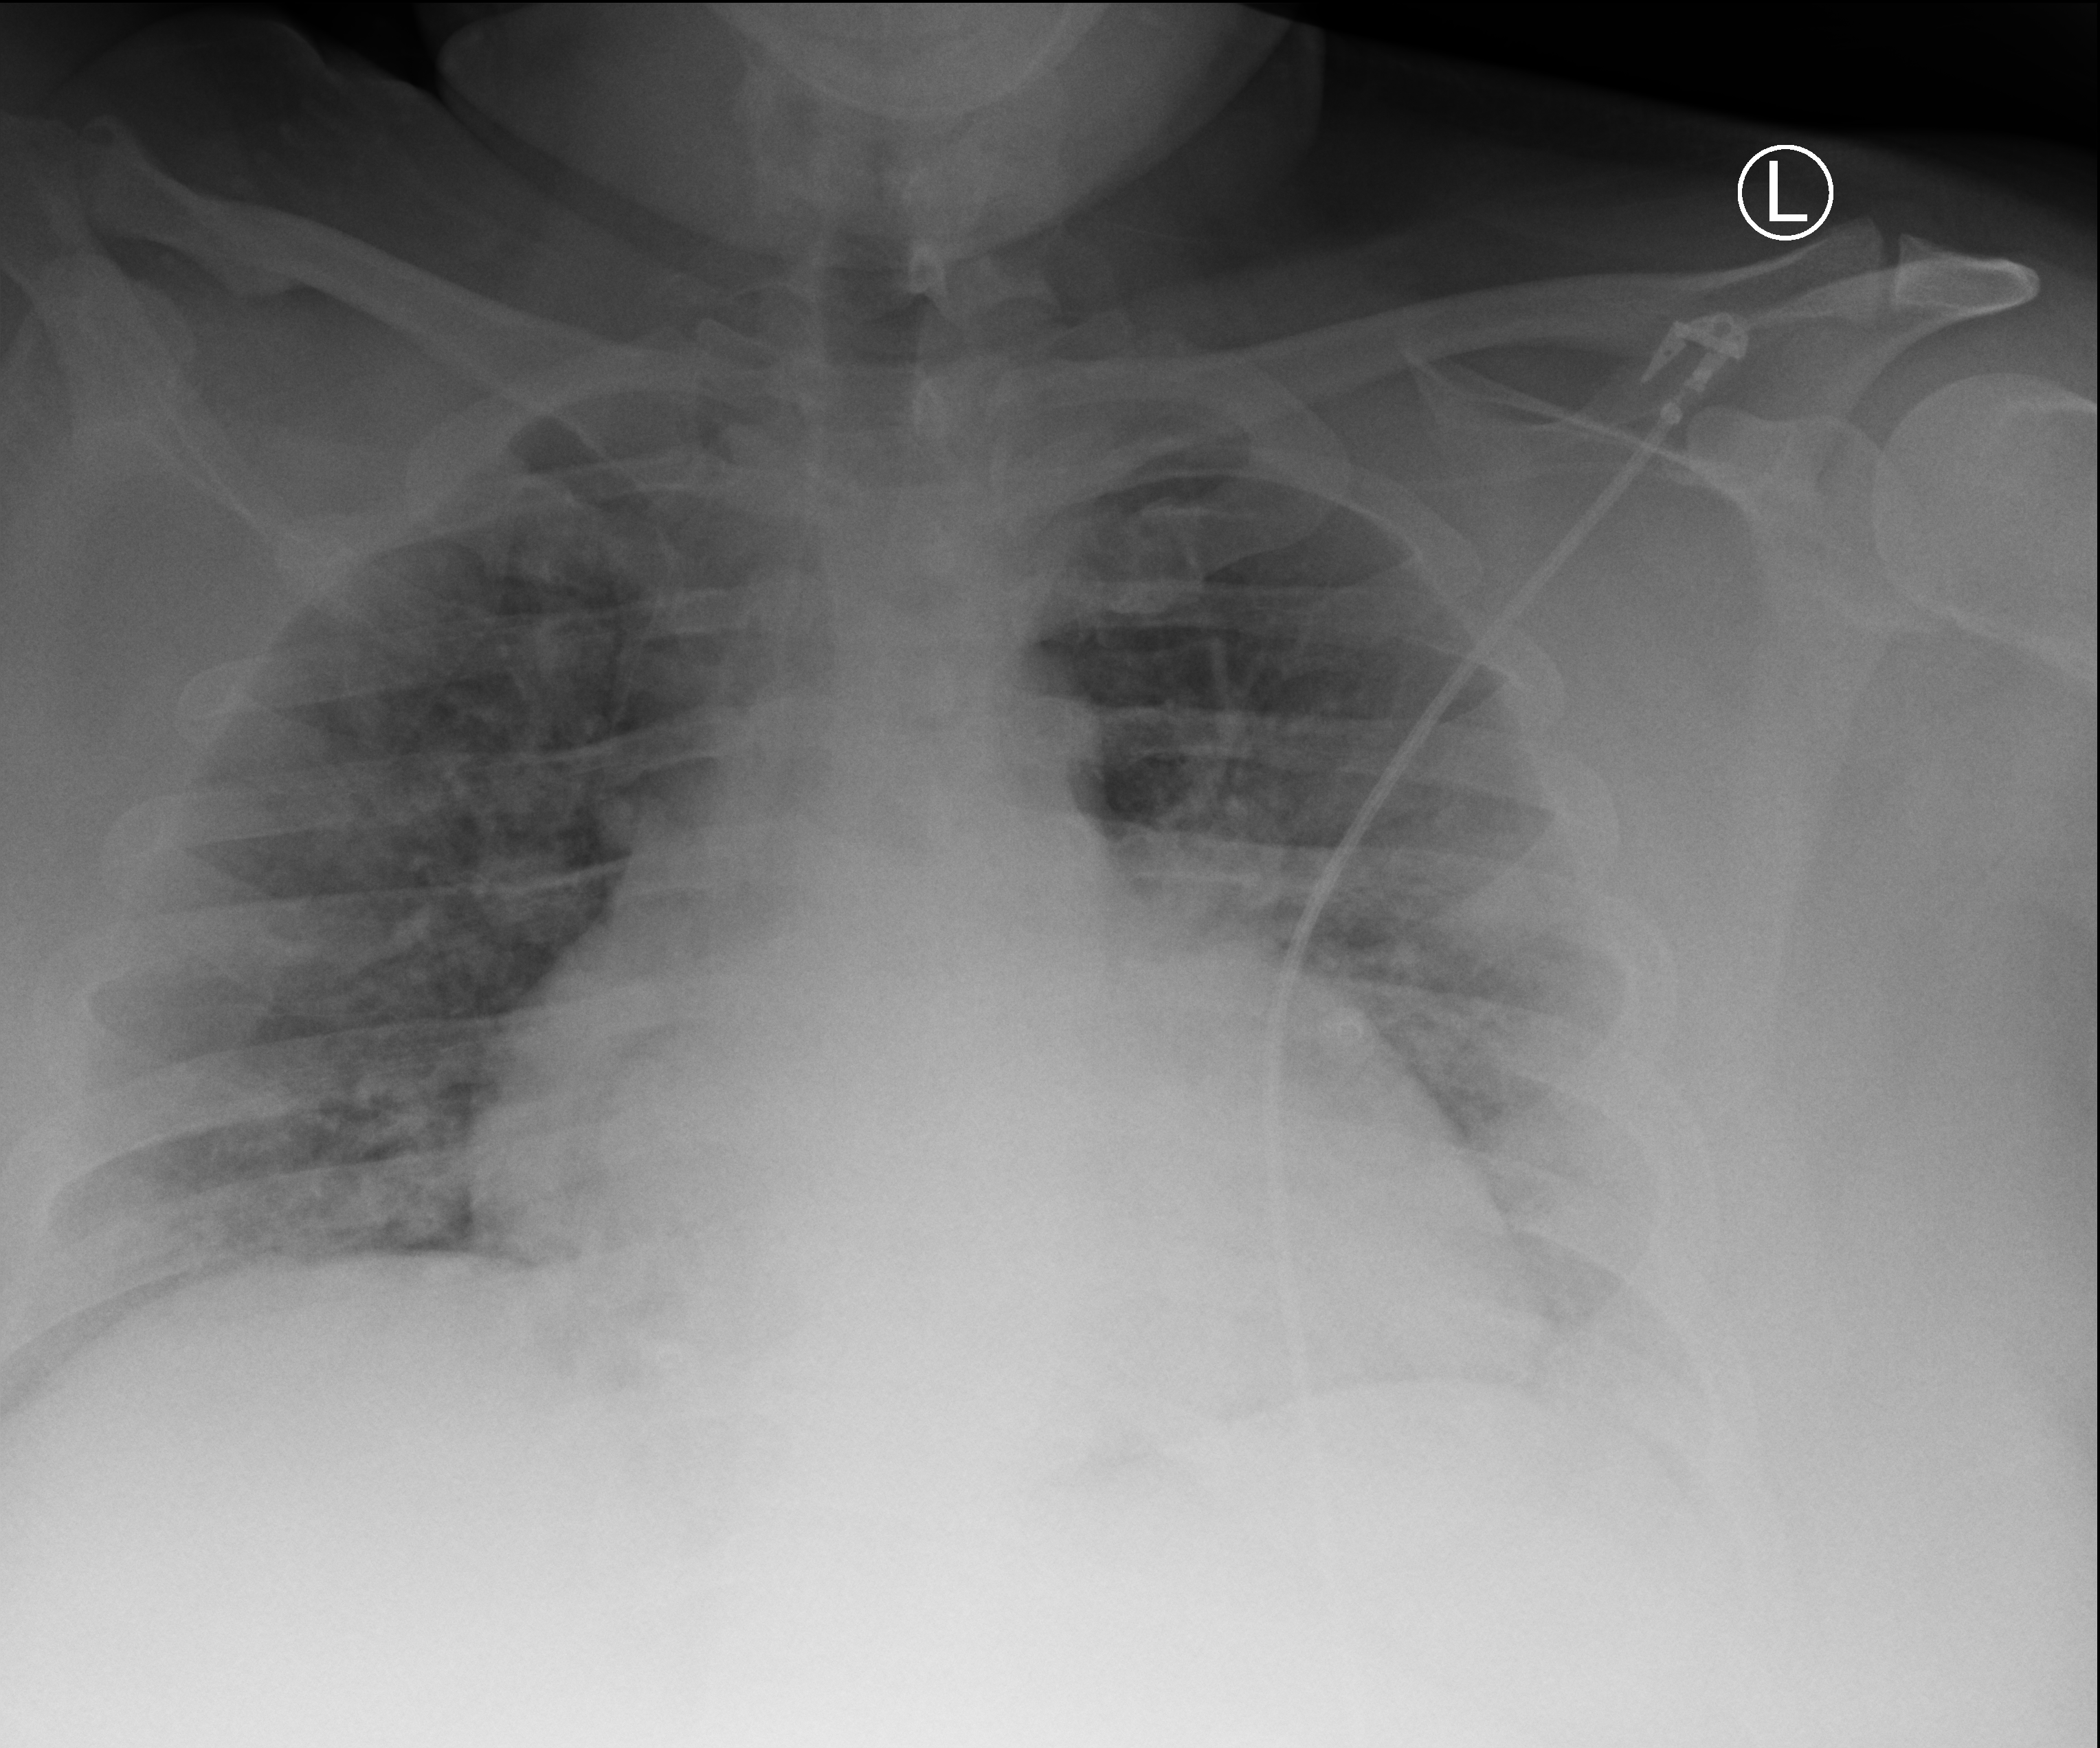
Chest X-ray (portable), anteroposterior (AP) projection. Male patient hospitalised with COVID-19, age 18–59 years.
From the hospital-stay record, not from the radiograph (when in the stay this image was taken is not recorded): COPD (admission record): no; chronic kidney disease (admission record): no; length of hospital stay: 19 days.